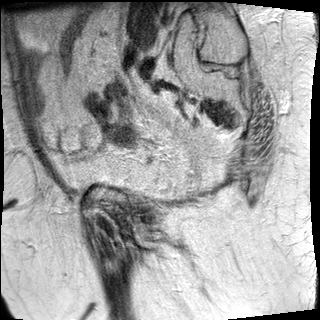
Pelvic MRI for cervical cancer, one sagittal slice; position 8 of 27 along the scan axis; T2-weighted; 1.5 T; TE 89 ms, TR 2740 ms; 320 × 320 image matrix, field of view 260 × 260 mm. Female patient, age 67 years.
Outlined on this slice (expert manual segmentation):
- uterus and cervix: box from (x=103, y=124) to (x=137, y=148) px